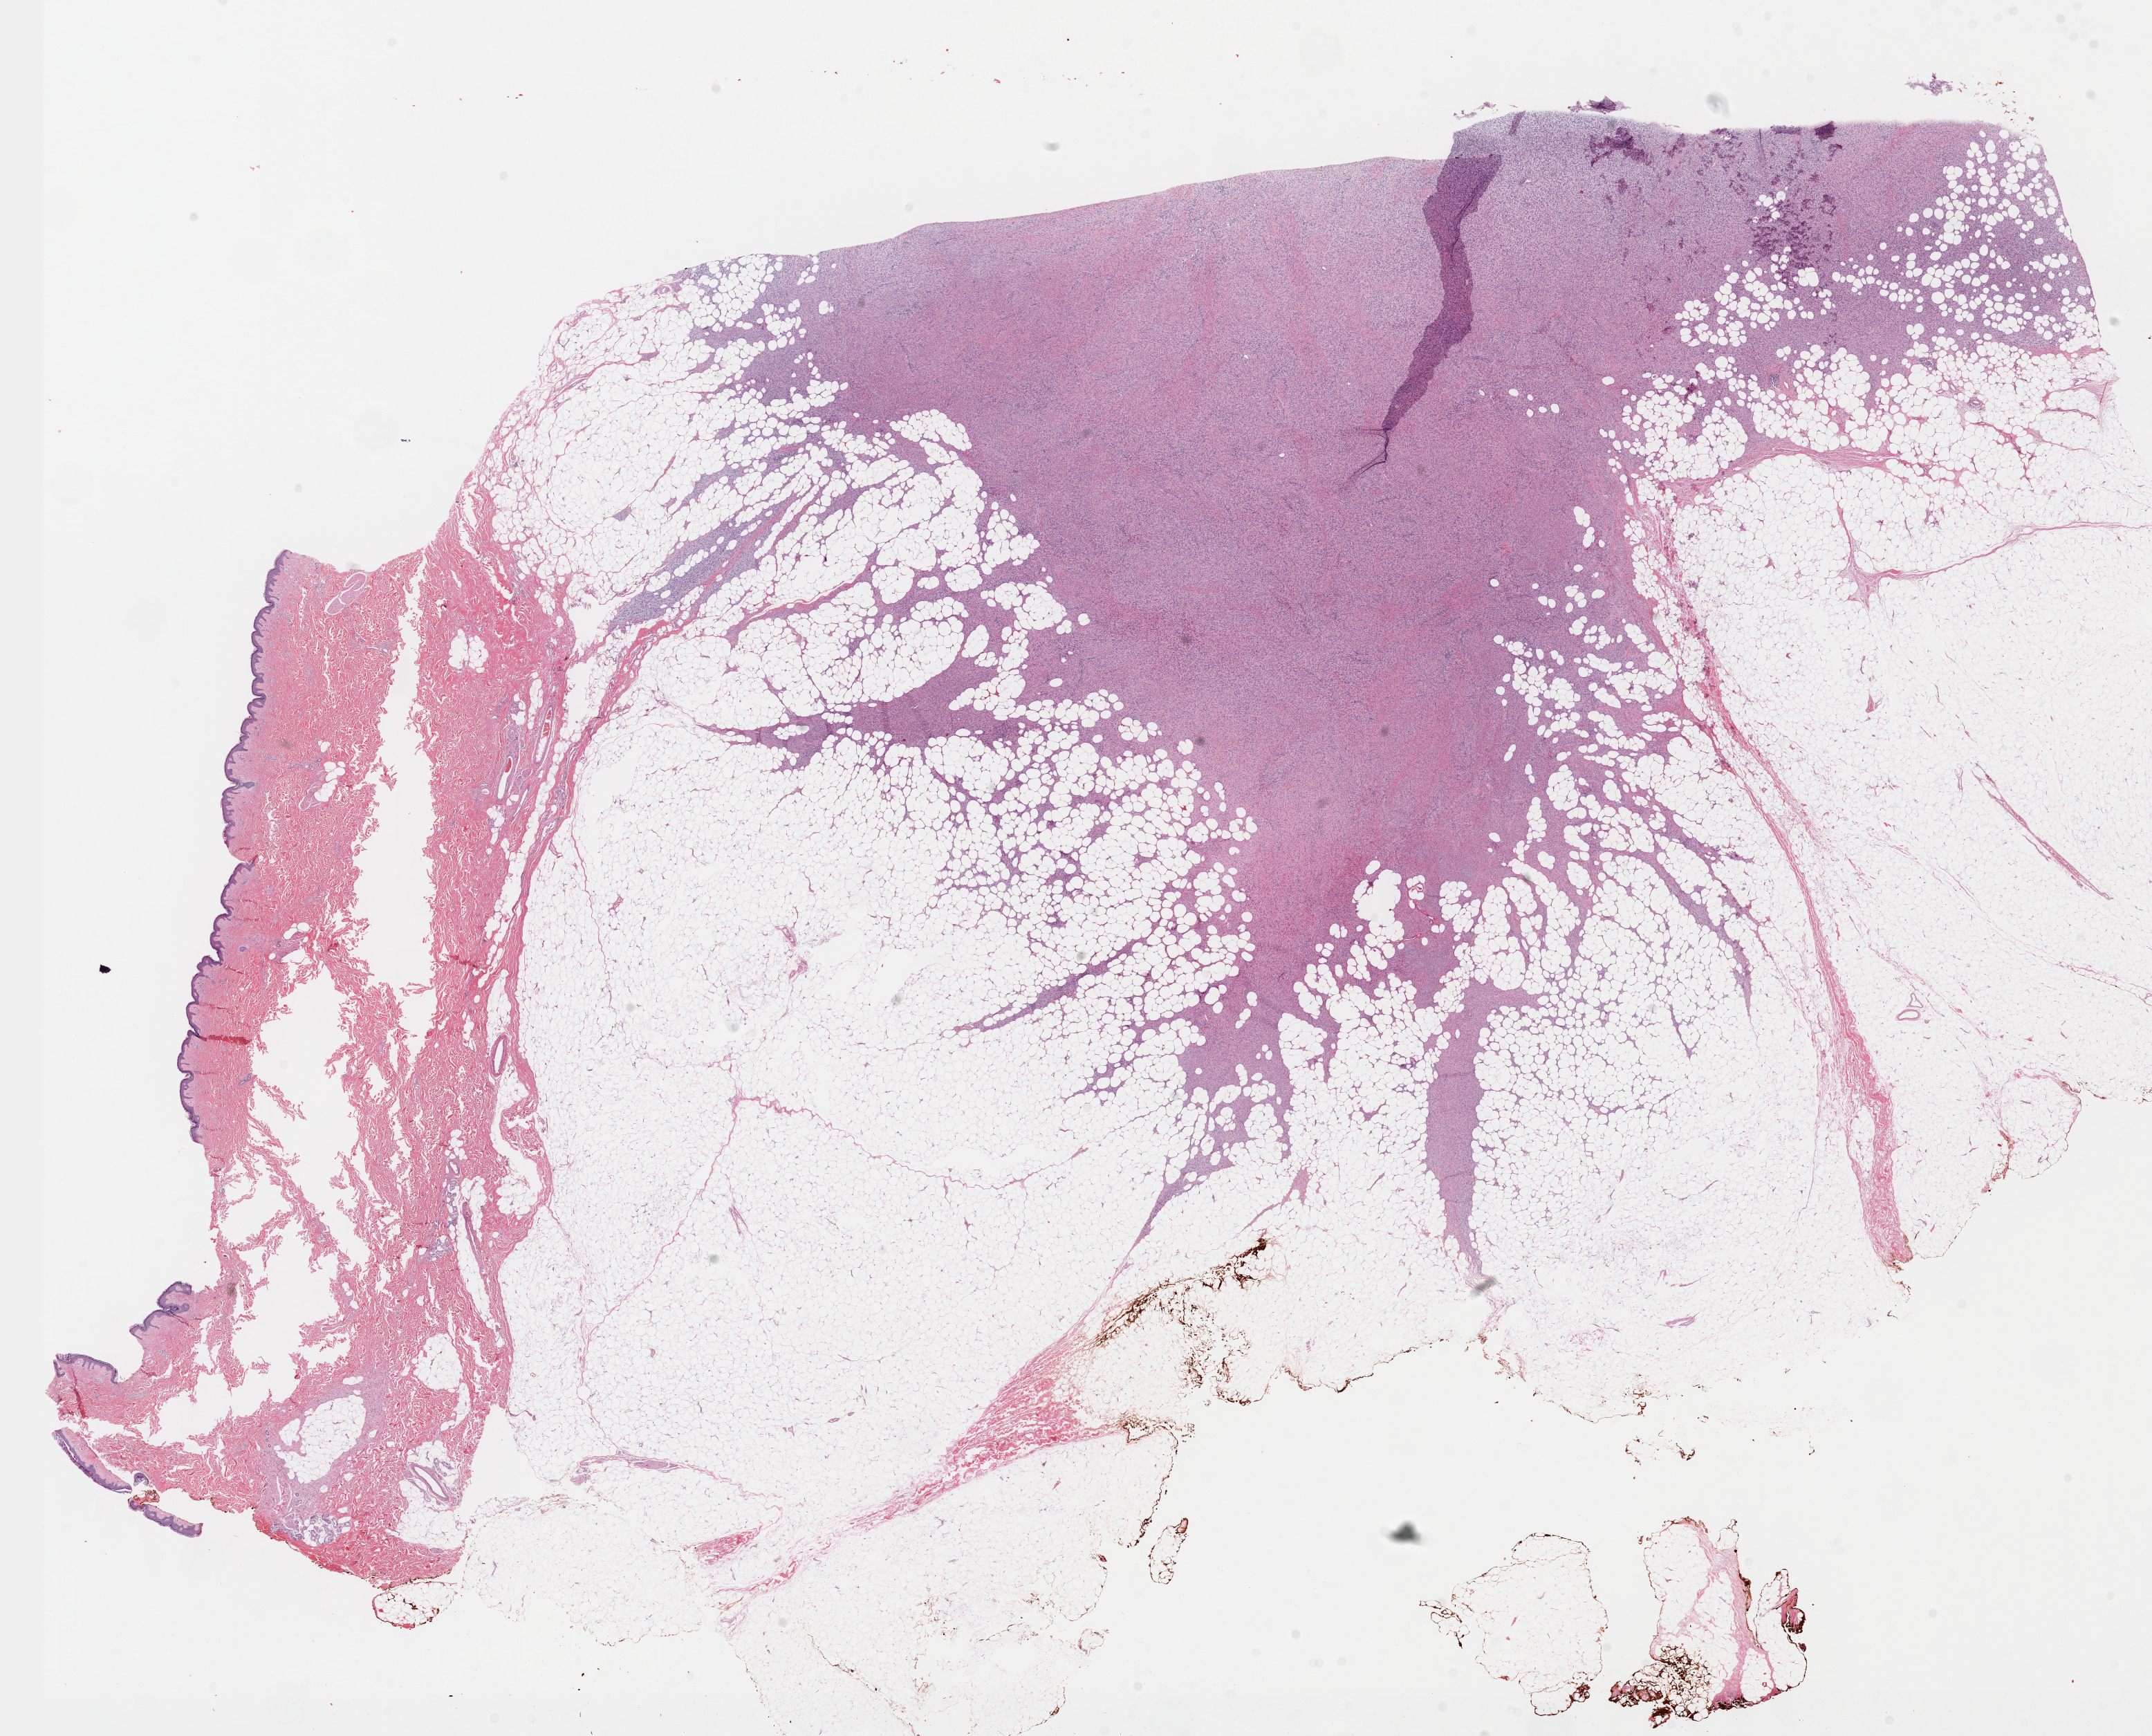
Digitized Hematoxylin and eosin (H&E) stained tissue section (whole slide), a low-resolution overview of the entire scanned area, about 25.1 x 20.3 mm (acquisition: 40x scan), FFPE section, connective, subcutaneous and other soft tissues, primary tumour sample. Female patient; age at initial diagnosis 68 years.
• diagnosis: Malignant peripheral nerve sheath tumor (connective, subcutaneous and other soft tissues of trunk, NOS)